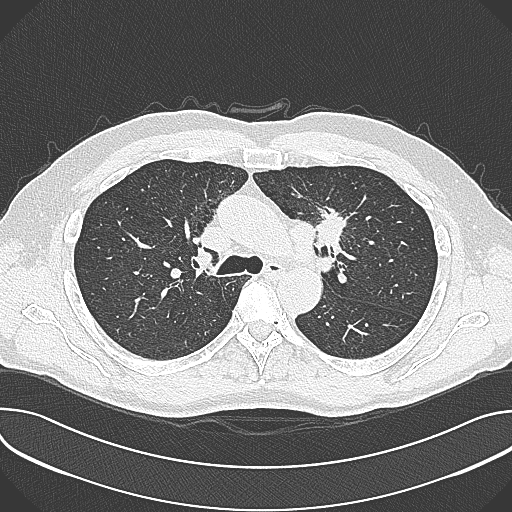
Axial slice from a low-dose chest CT screening exam; baseline annual screen; lung window (W 1500 / L -600 HU); slice 108 of 361 in the series. Male participant, aged 59 years at enrolment. Current smoker at enrolment.
Lesion marked by an expert reader, bounding box [x1, y1, x2, y2] px = [302, 195, 362, 257]. The screening reader recorded 2 non-calcified nodules or masses ≥4 mm on this exam (left upper lobe, left upper lobe); which of them this box marks is not recorded. Later outcome: lung cancer diagnosed 21 days after this screen — non-small cell carcinoma, left upper lobe, poorly differentiated (G3), stage IIIA (AJCC 6th edition), 35 mm at pathology.